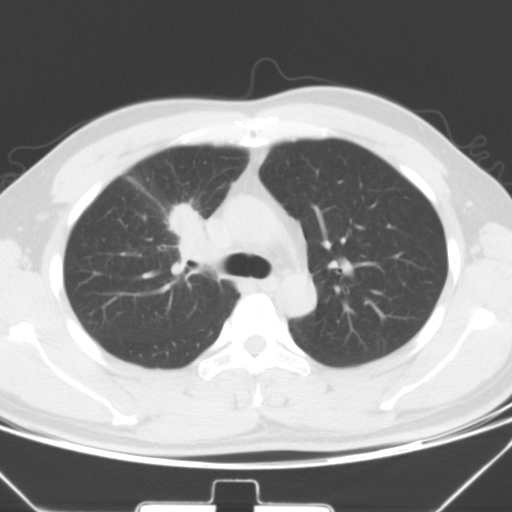
Chest CT, one axial slice. Position 41 of 60 along the scan axis. Lung window (W 1500 / L -600 HU). 512 × 512 image matrix. Male patient, age 35 years. From the clinical record (not read from this slice): clinical TNM (as recorded): T1c N1 M1b.
Outlined on this slice (rectangle marked by the reading radiologist):
- lung tumour (recorded histology: adenocarcinoma): box from (x=168, y=196) to (x=225, y=271) px